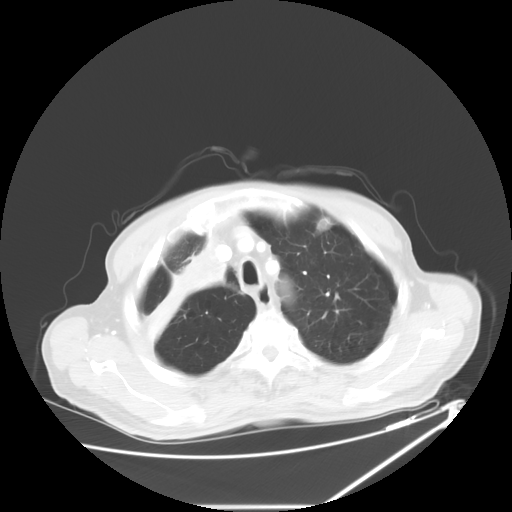
Chest CT, one axial slice; position 50 of 60 along the scan axis; reconstruction kernel STANDARD; 120 kVp; lung window (W 1500 / L -600 HU); 512 × 512 image matrix, field of view 410 × 410 mm. Male patient, age 73 years. Case-level facts recorded for this patient, not image findings: clinical TNM (as recorded): T2a N1 M0.
Annotated regions visible in this slice (bounding box drawn by a radiologist):
- lung tumour (recorded histology: squamous cell carcinoma): box from (x=142, y=237) to (x=228, y=348) px